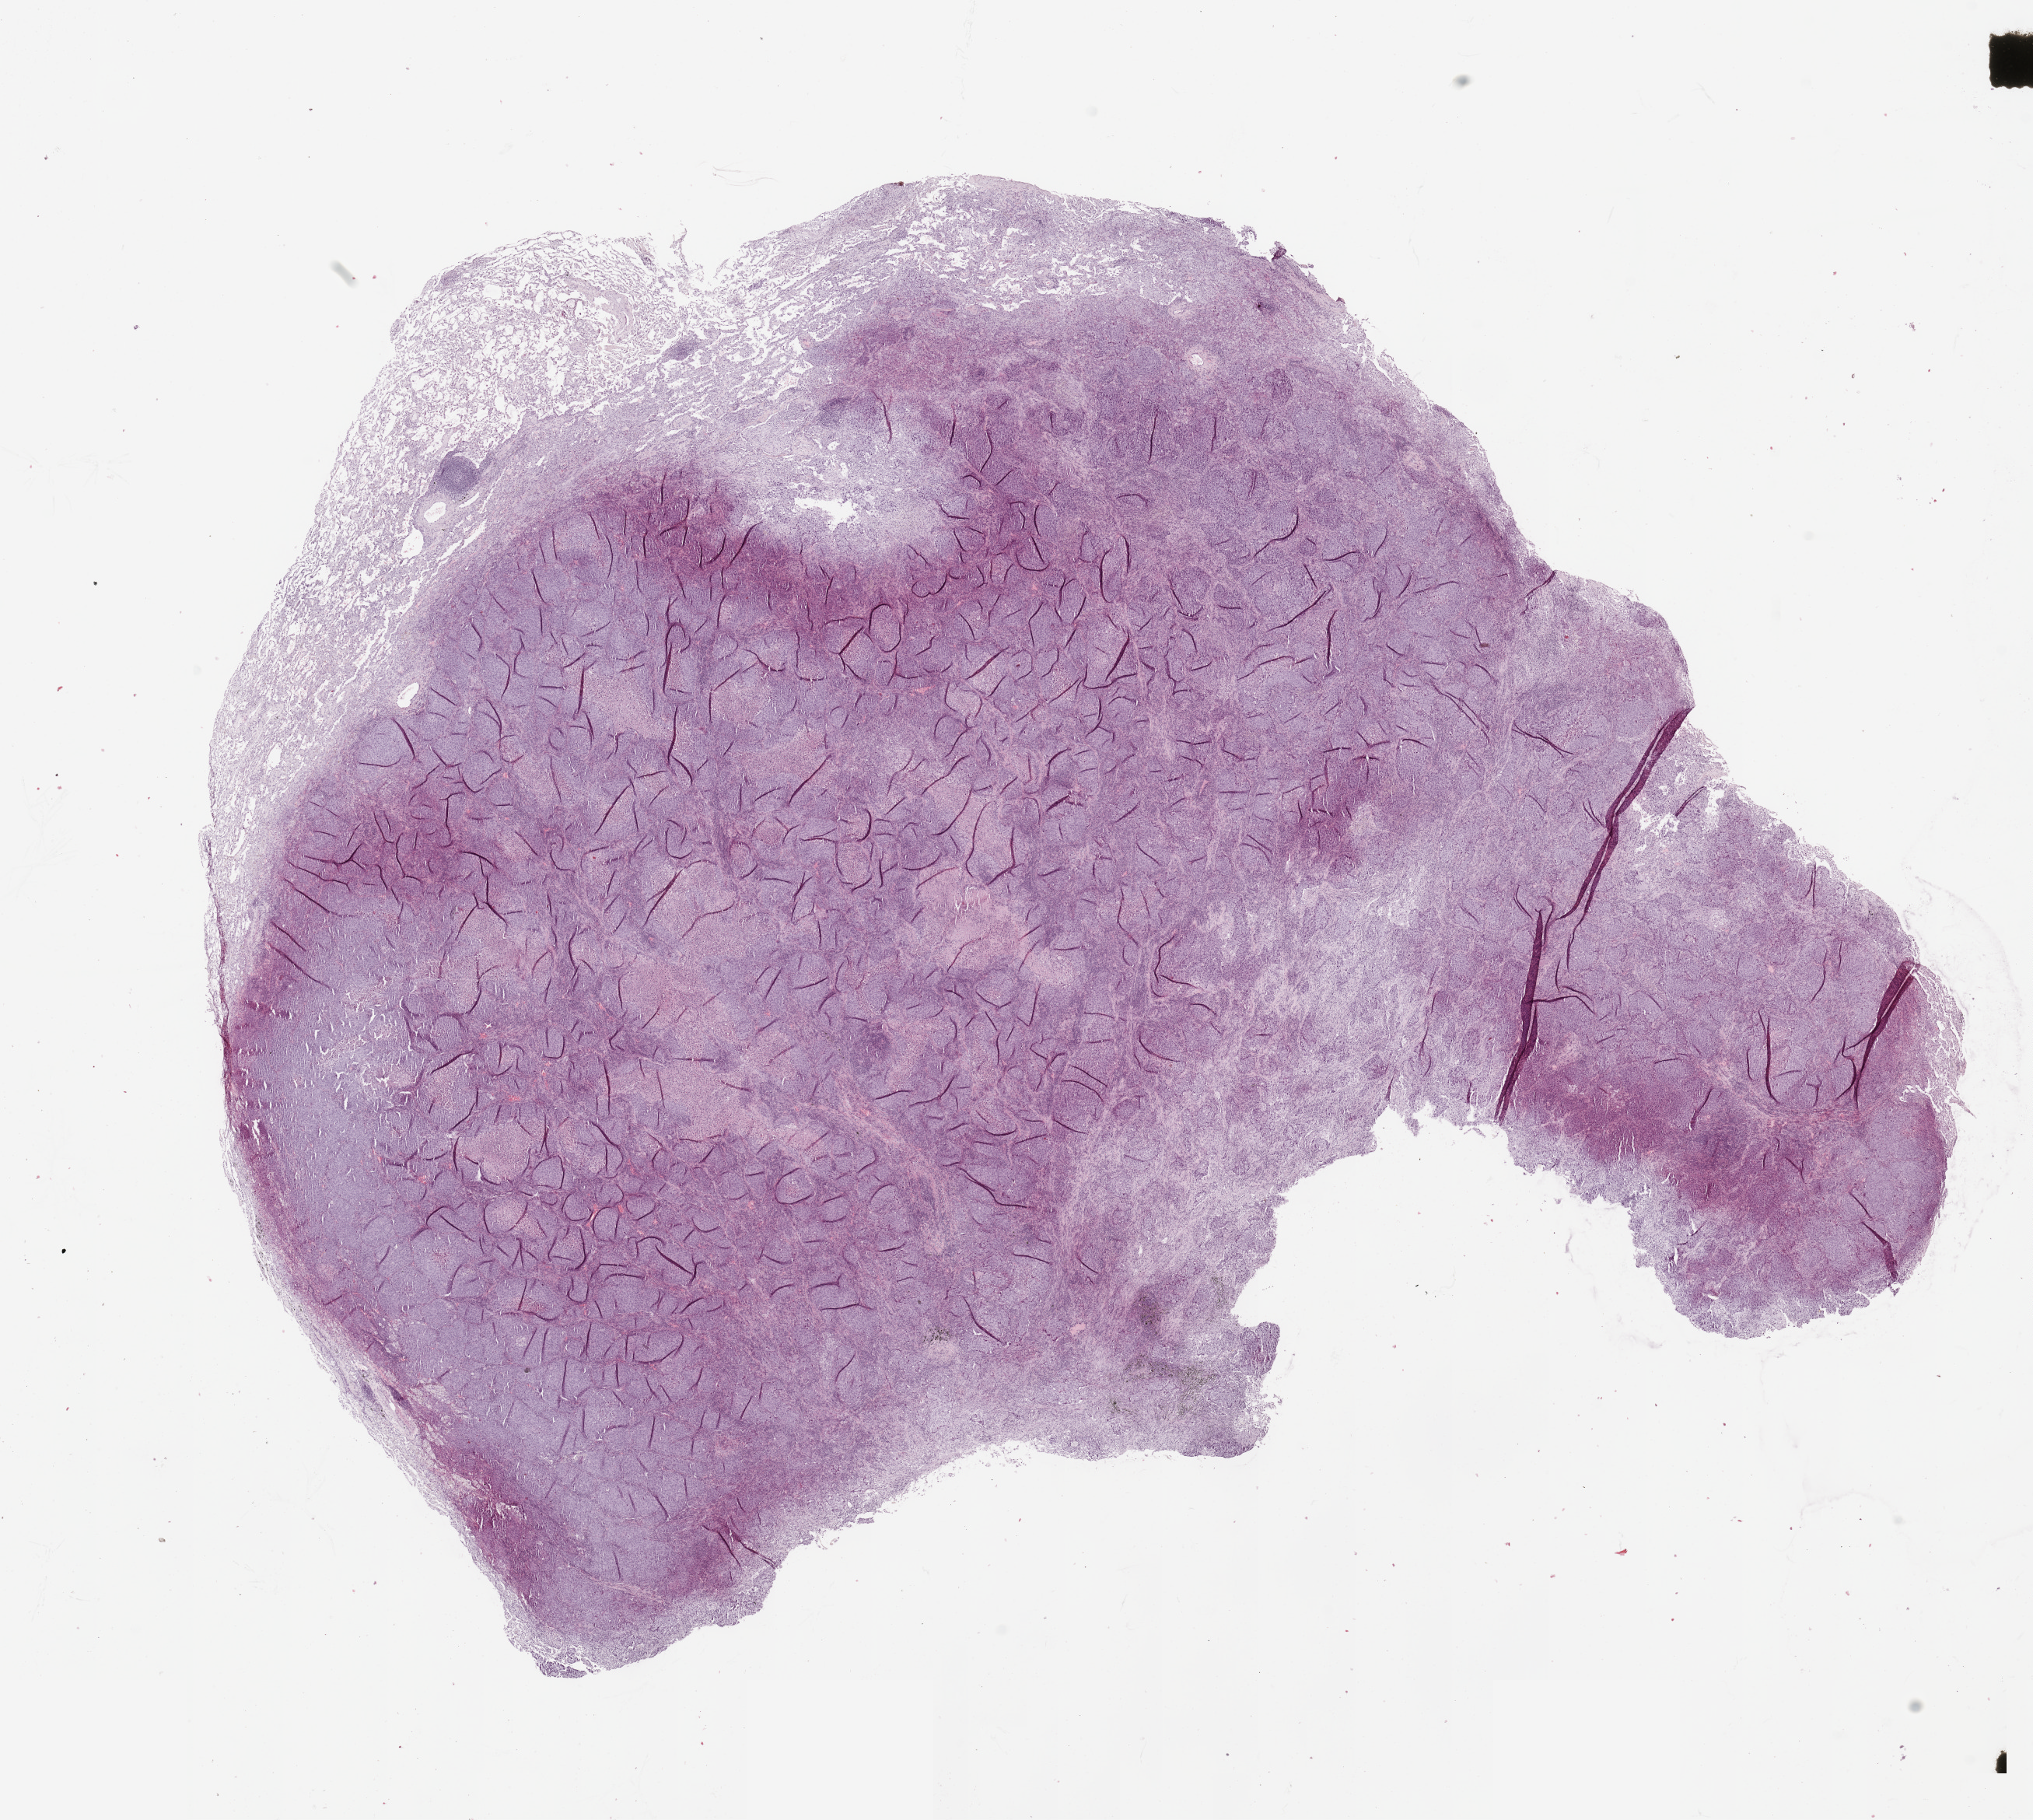
Whole-slide histology image, H&E — a low-resolution overview of the entire scanned area, about 20.7 x 18.5 mm (from a 20x scan). Tumour tissue sample, sampled site: lung. Patient: male, age 61 years. Histologic grade: G2 (moderately differentiated). Slide review estimates, as recorded: tumour nuclei 75%, necrosis 15%.
Diagnosis: Squamous cell carcinoma, NOS. Primary tumour site (as recorded): right upper lobe.